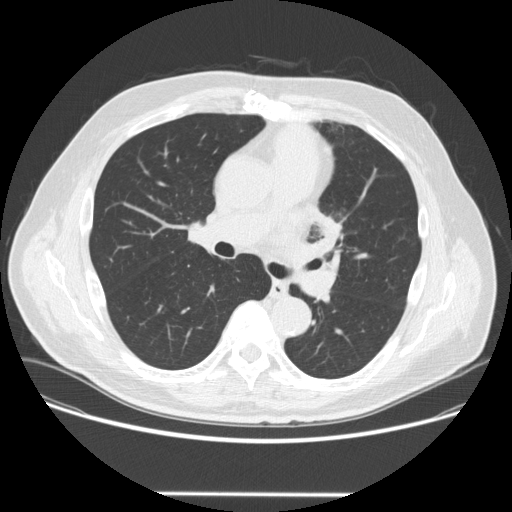
Low-dose screening chest CT, one axial slice; lung window (W 1500 / L -600 HU); 512 × 512 image matrix, field of view 400 × 400 mm.
Annotated regions visible in this slice (manually delineated by an expert):
- lesion 1 (tumor, upper lobe of left lung): bounding box [x1, y1, x2, y2] px = [321, 219, 341, 241]